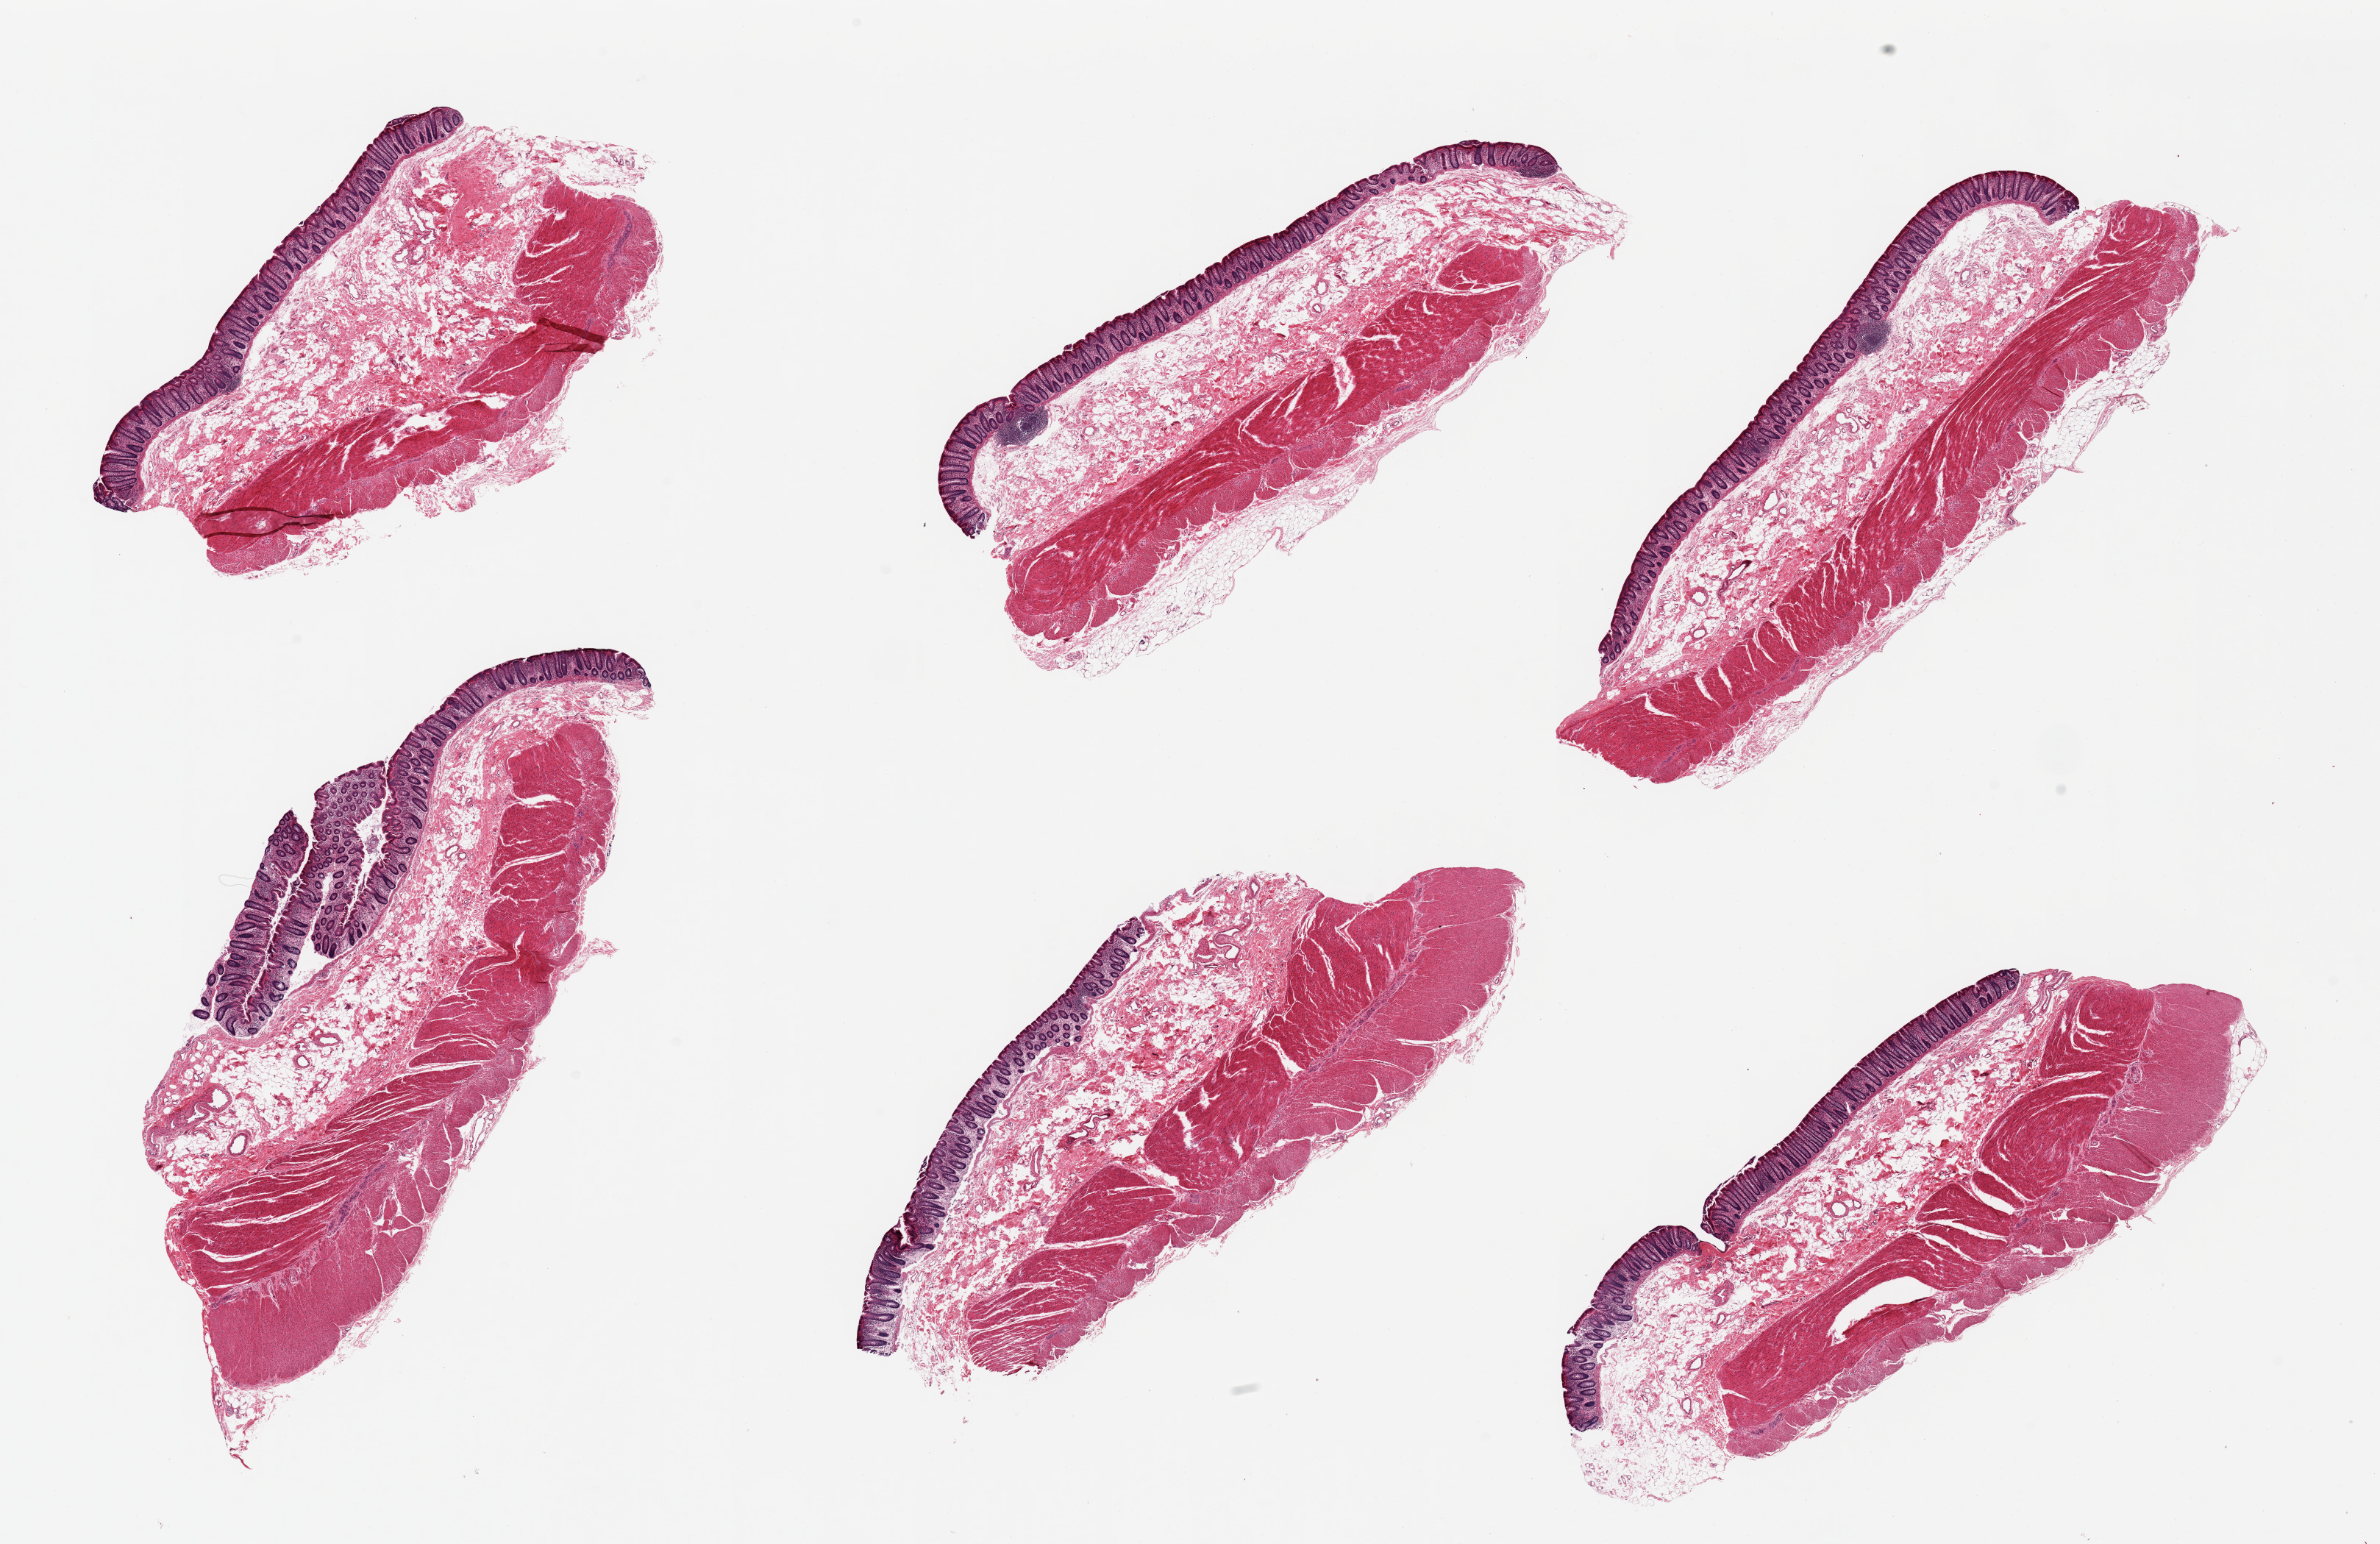
Hematoxylin and eosin (H&E) whole-slide image, brightfield, low-resolution overview of the scanned area, about 25.6 x 16.6 mm, PAXgene-fixed, paraffin-embedded tissue, sampled site (target tissue): transverse colon, donor tissue sample. Donor sex: male.
- reviewer comment on this tissue sample: 6 pieces